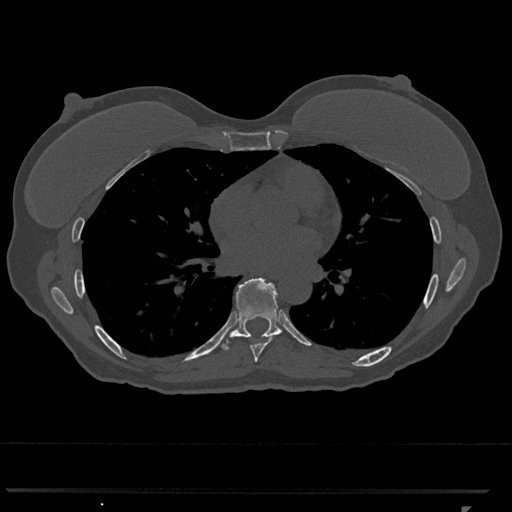
CT including the spine, one axial slice; slice 686 of 793 in the series (ordered by position); 120 kVp; bone window (W 1800 / L 400 HU); 512 × 512 image matrix. Female patient, age 62 years. Case-level facts recorded for this patient, not image findings: primary cancer: renal.
Outlined on this slice (semi-automatic segmentation, software-assisted and operator-edited):
- T7 vertebra: bounding box <247,335,274,362> (left, top, right, bottom; pixels)
- T8 vertebra: <219,278,283,350>